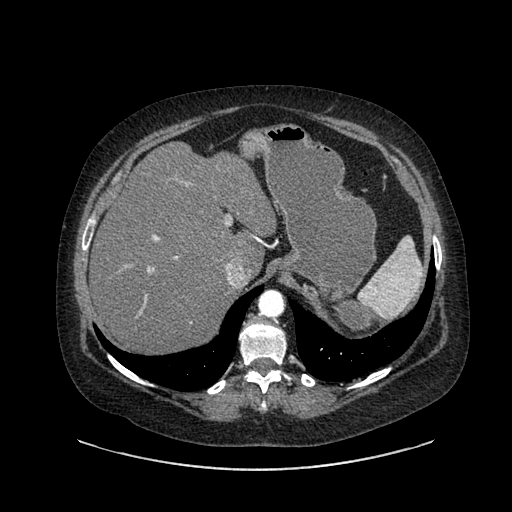
Contrast-enhanced abdominal CT, one axial slice; position 640 of 769 along the scan axis; reconstruction kernel SOFT; 120 kVp; intravenous contrast given; soft-tissue window (W 400 / L 40 HU); 0.62 mm slice thickness; 512 × 512 image matrix, field of view 460 × 460 mm. Patient: female, 61 years. From the clinical record (not read from this slice): diagnosis: adrenocortical carcinoma; tumour side: left adrenal; tumour size at pathology: 13 cm; Ki-67 index: 79 %; stage (as recorded): 2.
Annotated regions visible in this slice (semi-automatically segmented with operator editing):
- mass: bounding box <324,295,373,338> (left, top, right, bottom; pixels)